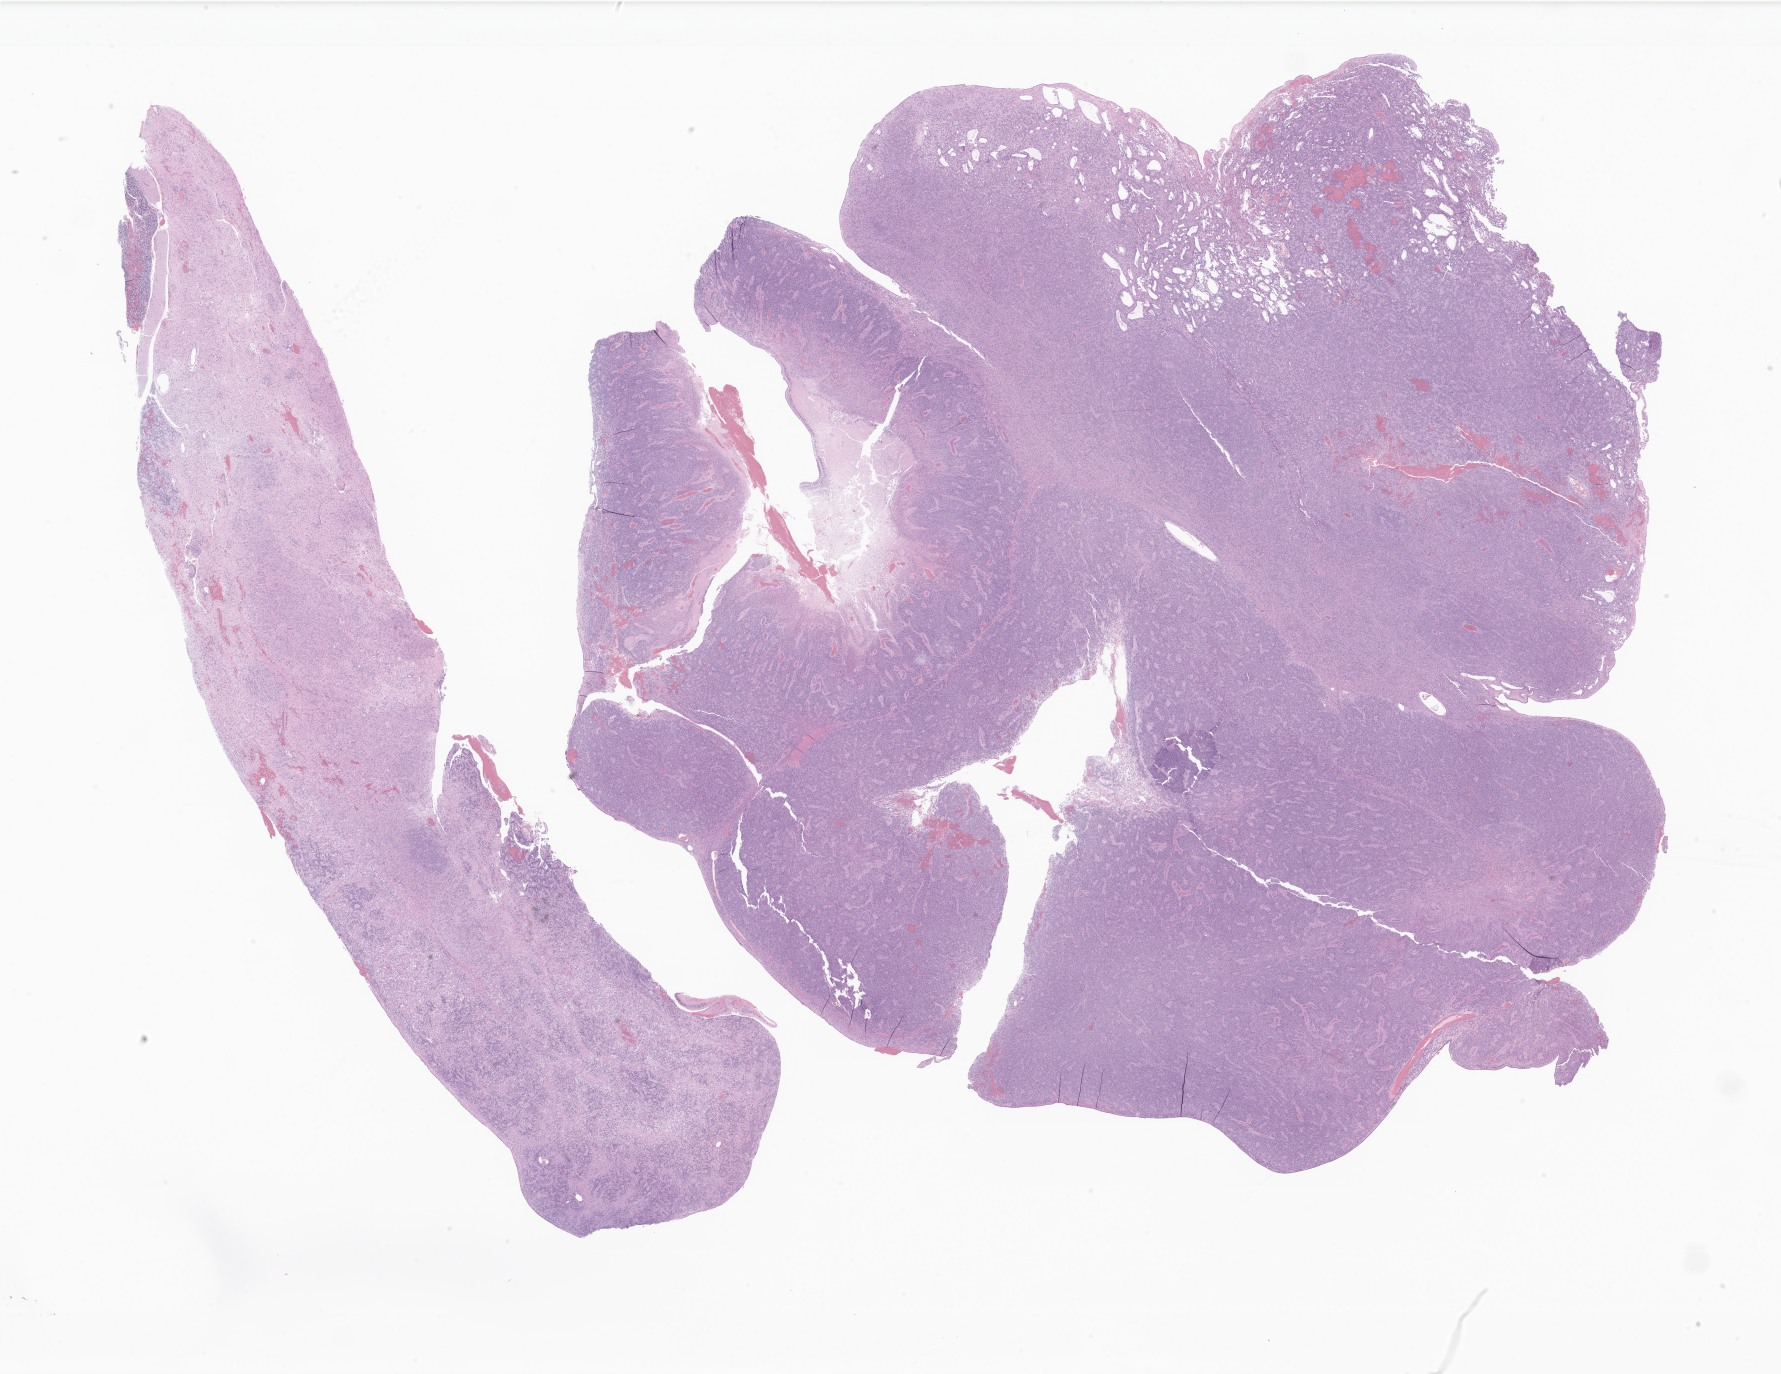
Whole-slide image, H&E stain of tumor tissue from the brain — whole scanned area (about 30.0 x 23.2 mm) shown as a low-resolution overview; formalin-fixed paraffin-embedded section. Patient male; age 740 days (about 2.0 years).
Recorded diagnosis: Ependymoma, NOS.